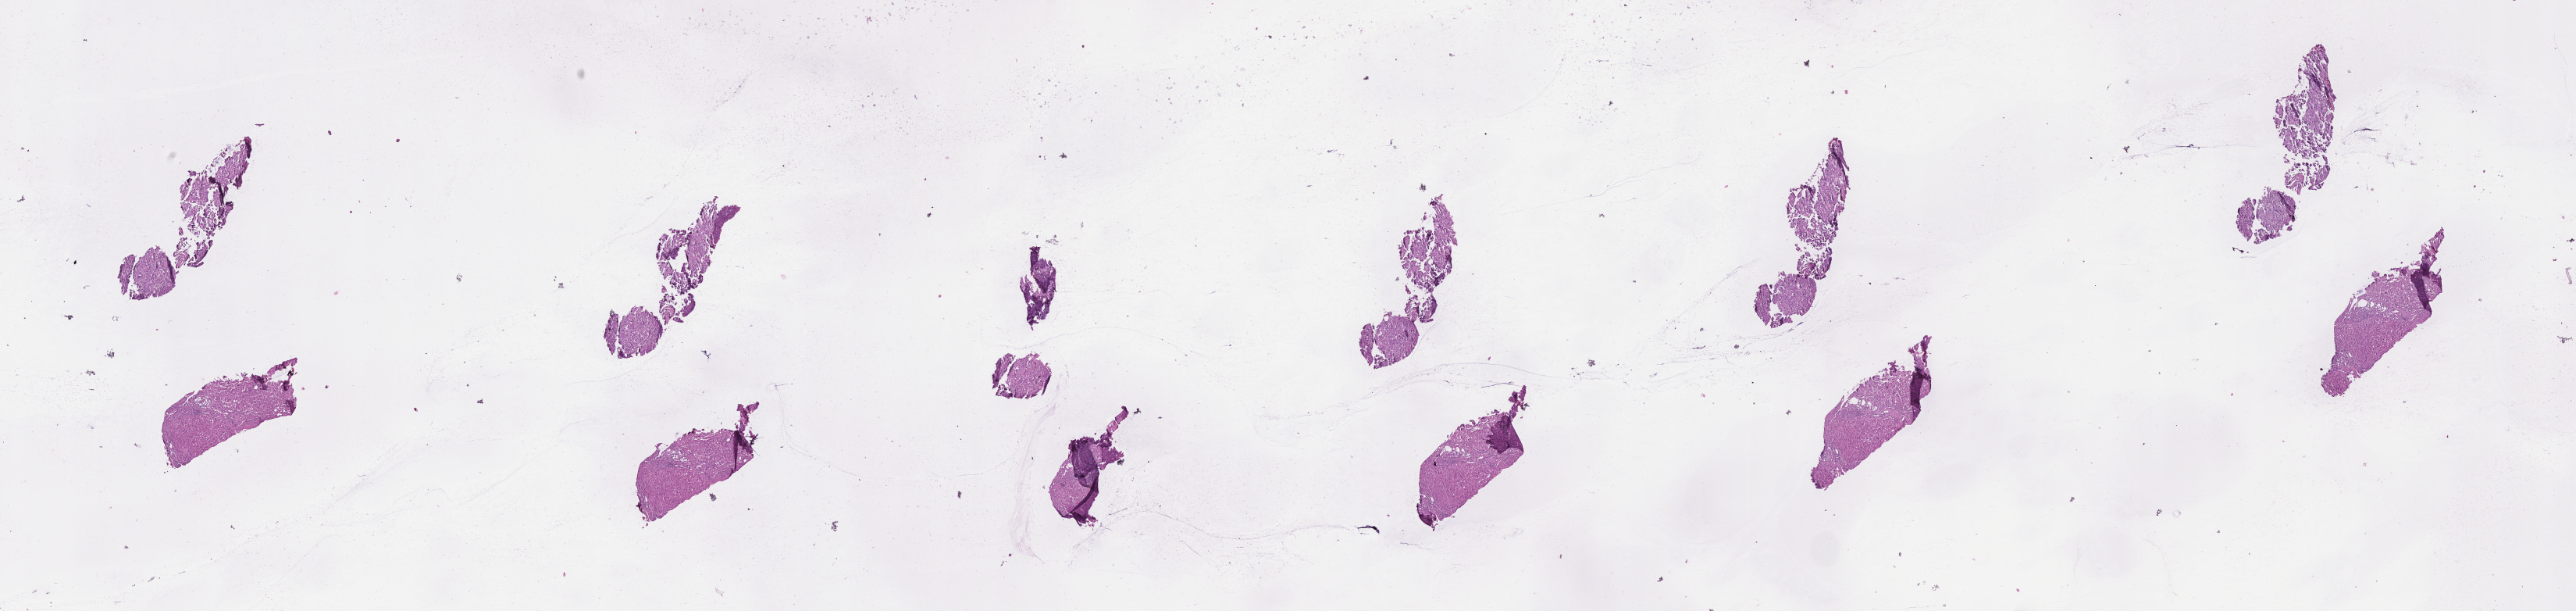
H&E-stained whole-slide image, shown as a low-resolution overview of the whole scanned area (about 26.7 x 6.3 mm). FFPE section. Sample: primary tumour, liver. Patient: male, age at initial diagnosis 64 years. Histologic grade: G1 (well differentiated).
Histologic diagnosis: Hepatocellular carcinoma, NOS. AJCC pathologic stage: I.